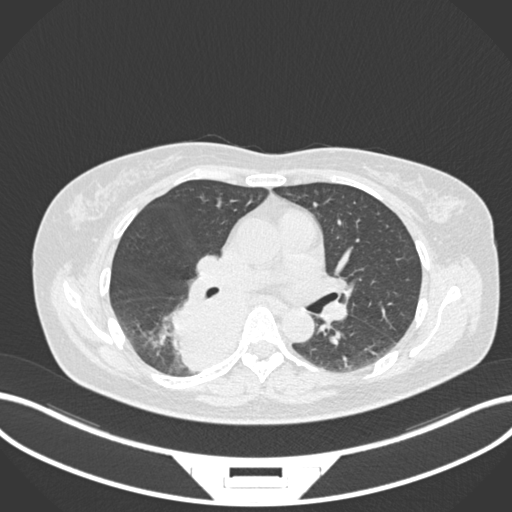
Chest CT, one axial slice; slice 600 of 677 in the series (ordered by position); reconstruction kernel B30f; 120 kVp; lung window (W 1500 / L -600 HU); 1 mm slice thickness; 512 × 512 image matrix, field of view 400 × 400 mm. Female patient, age 54 years. Case-level facts recorded for this patient, not image findings: clinical TNM (as recorded): T4 N0 M0.
Outlined on this slice (rectangle marked by the reading radiologist):
- lung tumour (recorded histology: adenocarcinoma): bounding box [x1, y1, x2, y2] px = [166, 286, 251, 377]